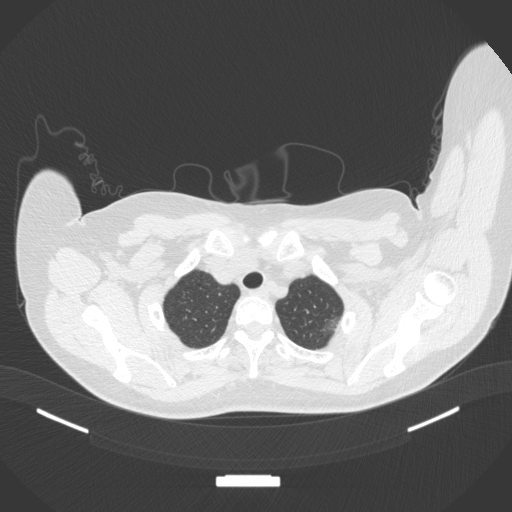
Chest CT, one axial slice; position 328 of 386 along the scan axis; 120 kVp; lung window (W 1500 / L -600 HU); 1 mm slice thickness; 512 × 512 image matrix, field of view 400 × 400 mm. Patient: female, 58 years. Case-level facts recorded for this patient, not image findings: clinical TNM (as recorded): T1c N0 M0.
Structures marked on this image (rectangle marked by the reading radiologist):
- lung tumour (recorded histology: adenocarcinoma): box from (x=319, y=314) to (x=345, y=339) px